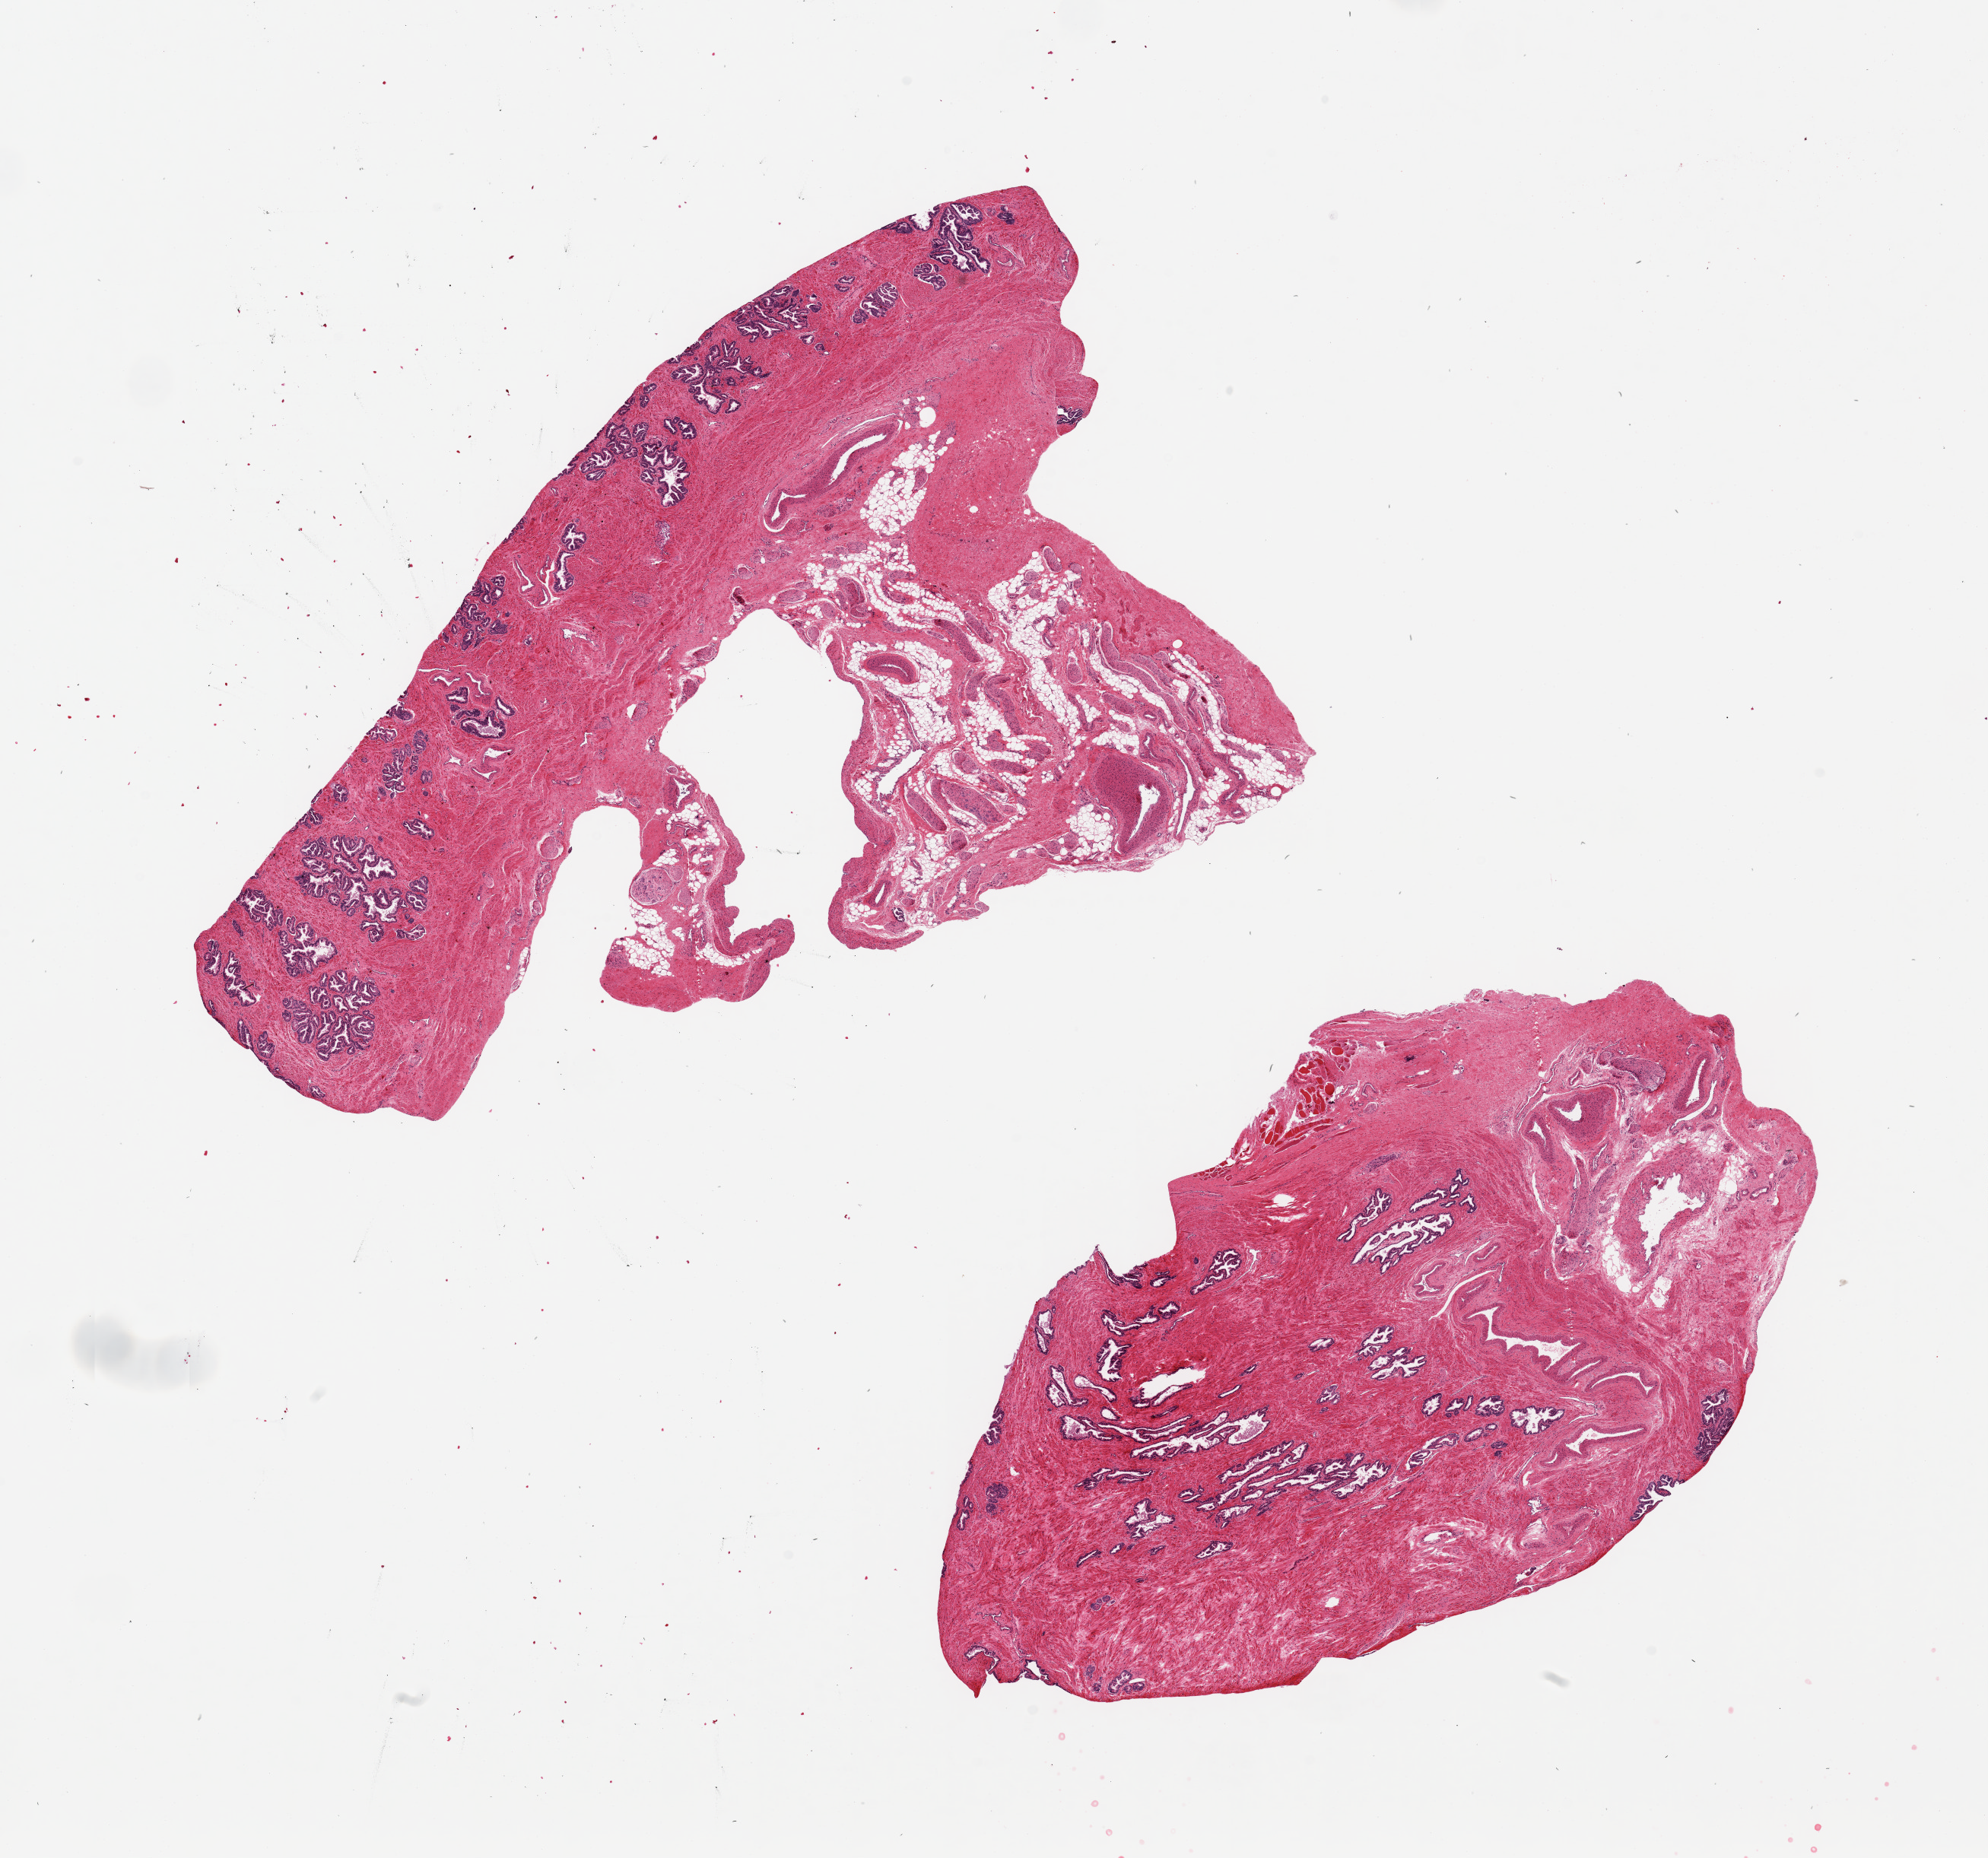
Digitized hematoxylin and eosin (H&E)-stained section, low-resolution overview of the scanned area, about 20.7 x 19.3 mm (slide scanned at 20x), PAXgene-fixed, paraffin-embedded tissue, target tissue: prostate, donor tissue sample. Donor sex: male.
Review note (as recorded): 2 pieces ~11x4mm, one with adherent fat/fibrous nubbin up to 5mm.